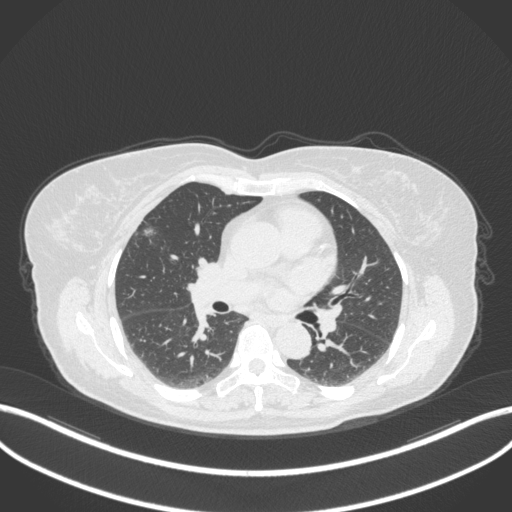
Chest CT, one axial slice; reconstruction kernel B31f; lung window (W 1500 / L -600 HU); 1 mm slice thickness; 512 × 512 image matrix, field of view 400 × 400 mm. Female patient, age 55 years. Case-level facts recorded for this patient, not image findings: clinical TNM (as recorded): T1b N0 M0; histopathological grade: G2.
Structures marked on this image (rectangle marked by the reading radiologist):
- lung tumour (recorded histology: adenocarcinoma): bounding box (x1, y1, x2, y2) in pixels: (143, 225, 158, 242)